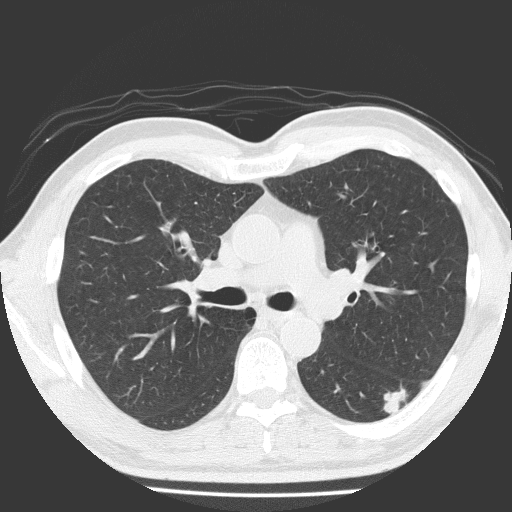
Low-dose screening chest CT, one axial slice. Slice 113 of 184 in the series (ordered by position). Reconstruction kernel FC51. Lung window (W 1500 / L -600 HU). 2 mm slice thickness. 512 × 512 image matrix.
Outlined on this slice (expert manual segmentation):
- lesion 1 (tumor, lower lobe of left lung): box from (x=383, y=384) to (x=409, y=416) px